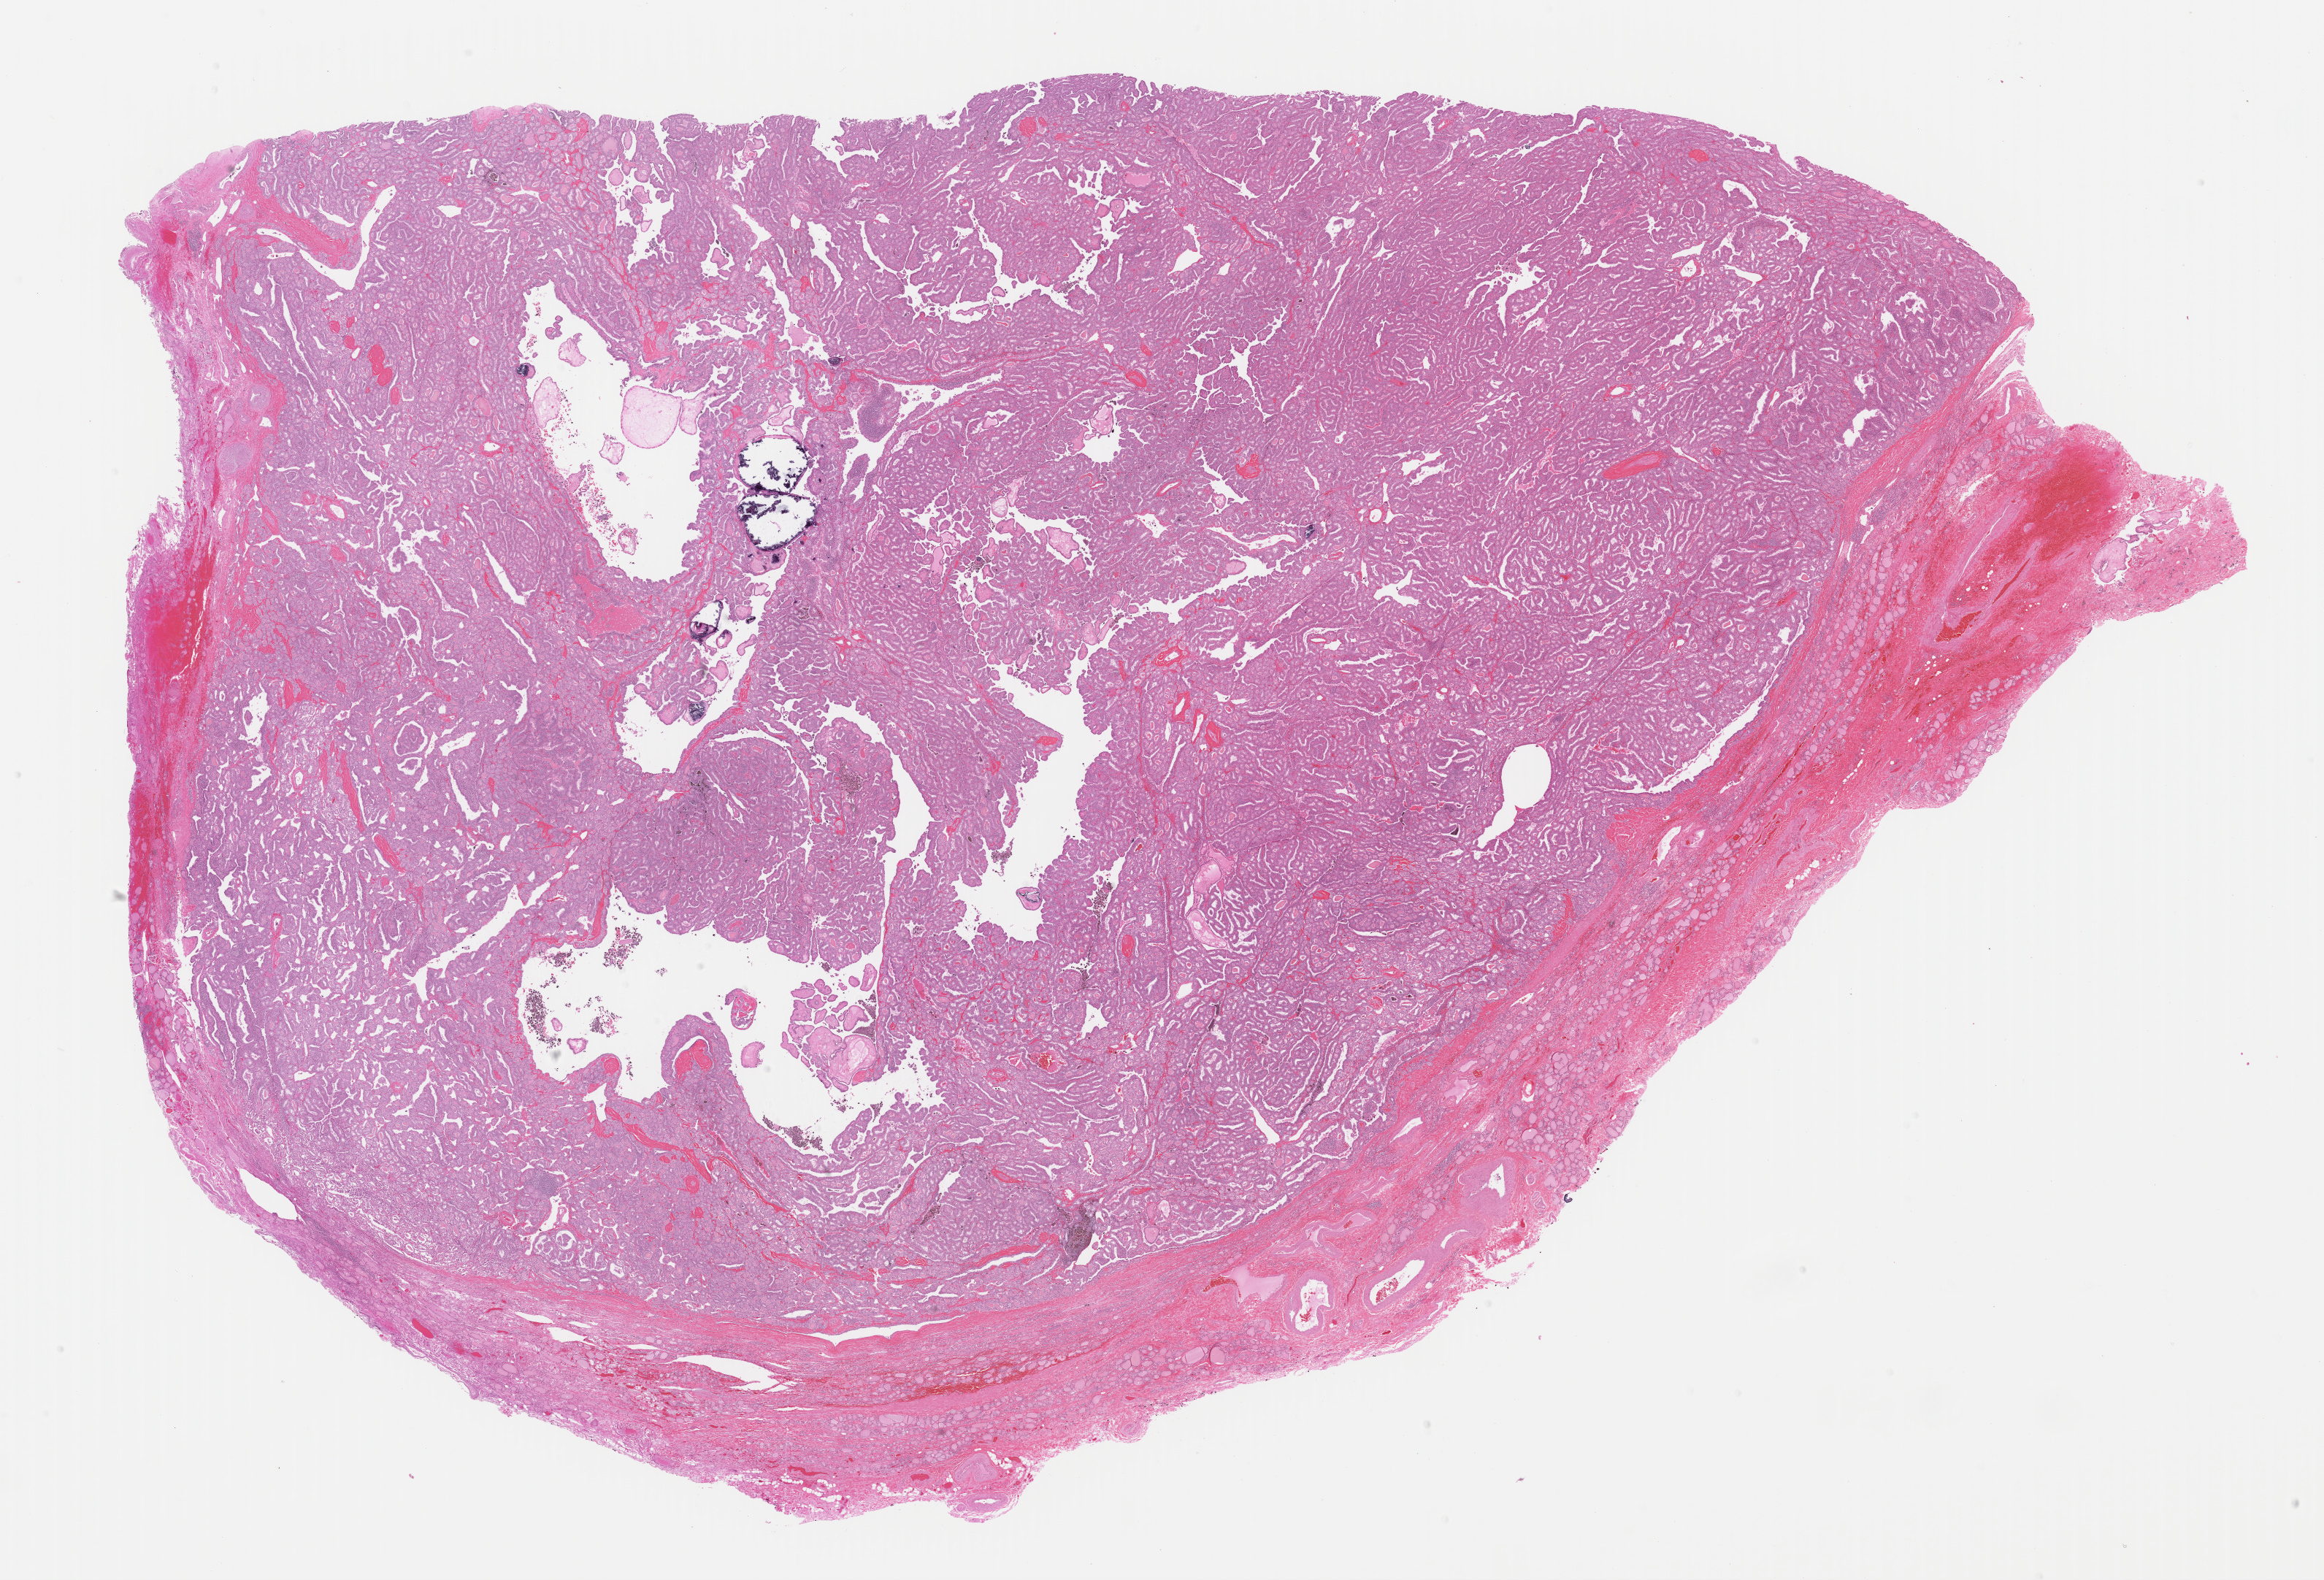
Whole-slide histology image, Hematoxylin and eosin (H&E) stained, a low-resolution overview of the entire scanned area, about 25.1 x 17.1 mm (acquisition: 40x scan); formalin-fixed paraffin-embedded (FFPE) diagnostic section; thyroid, primary tumour sample. Female patient; age at initial diagnosis 78 years.
AJCC pathologic stage: II (6th edition). Pathologic diagnosis: Papillary adenocarcinoma, NOS (thyroid gland).